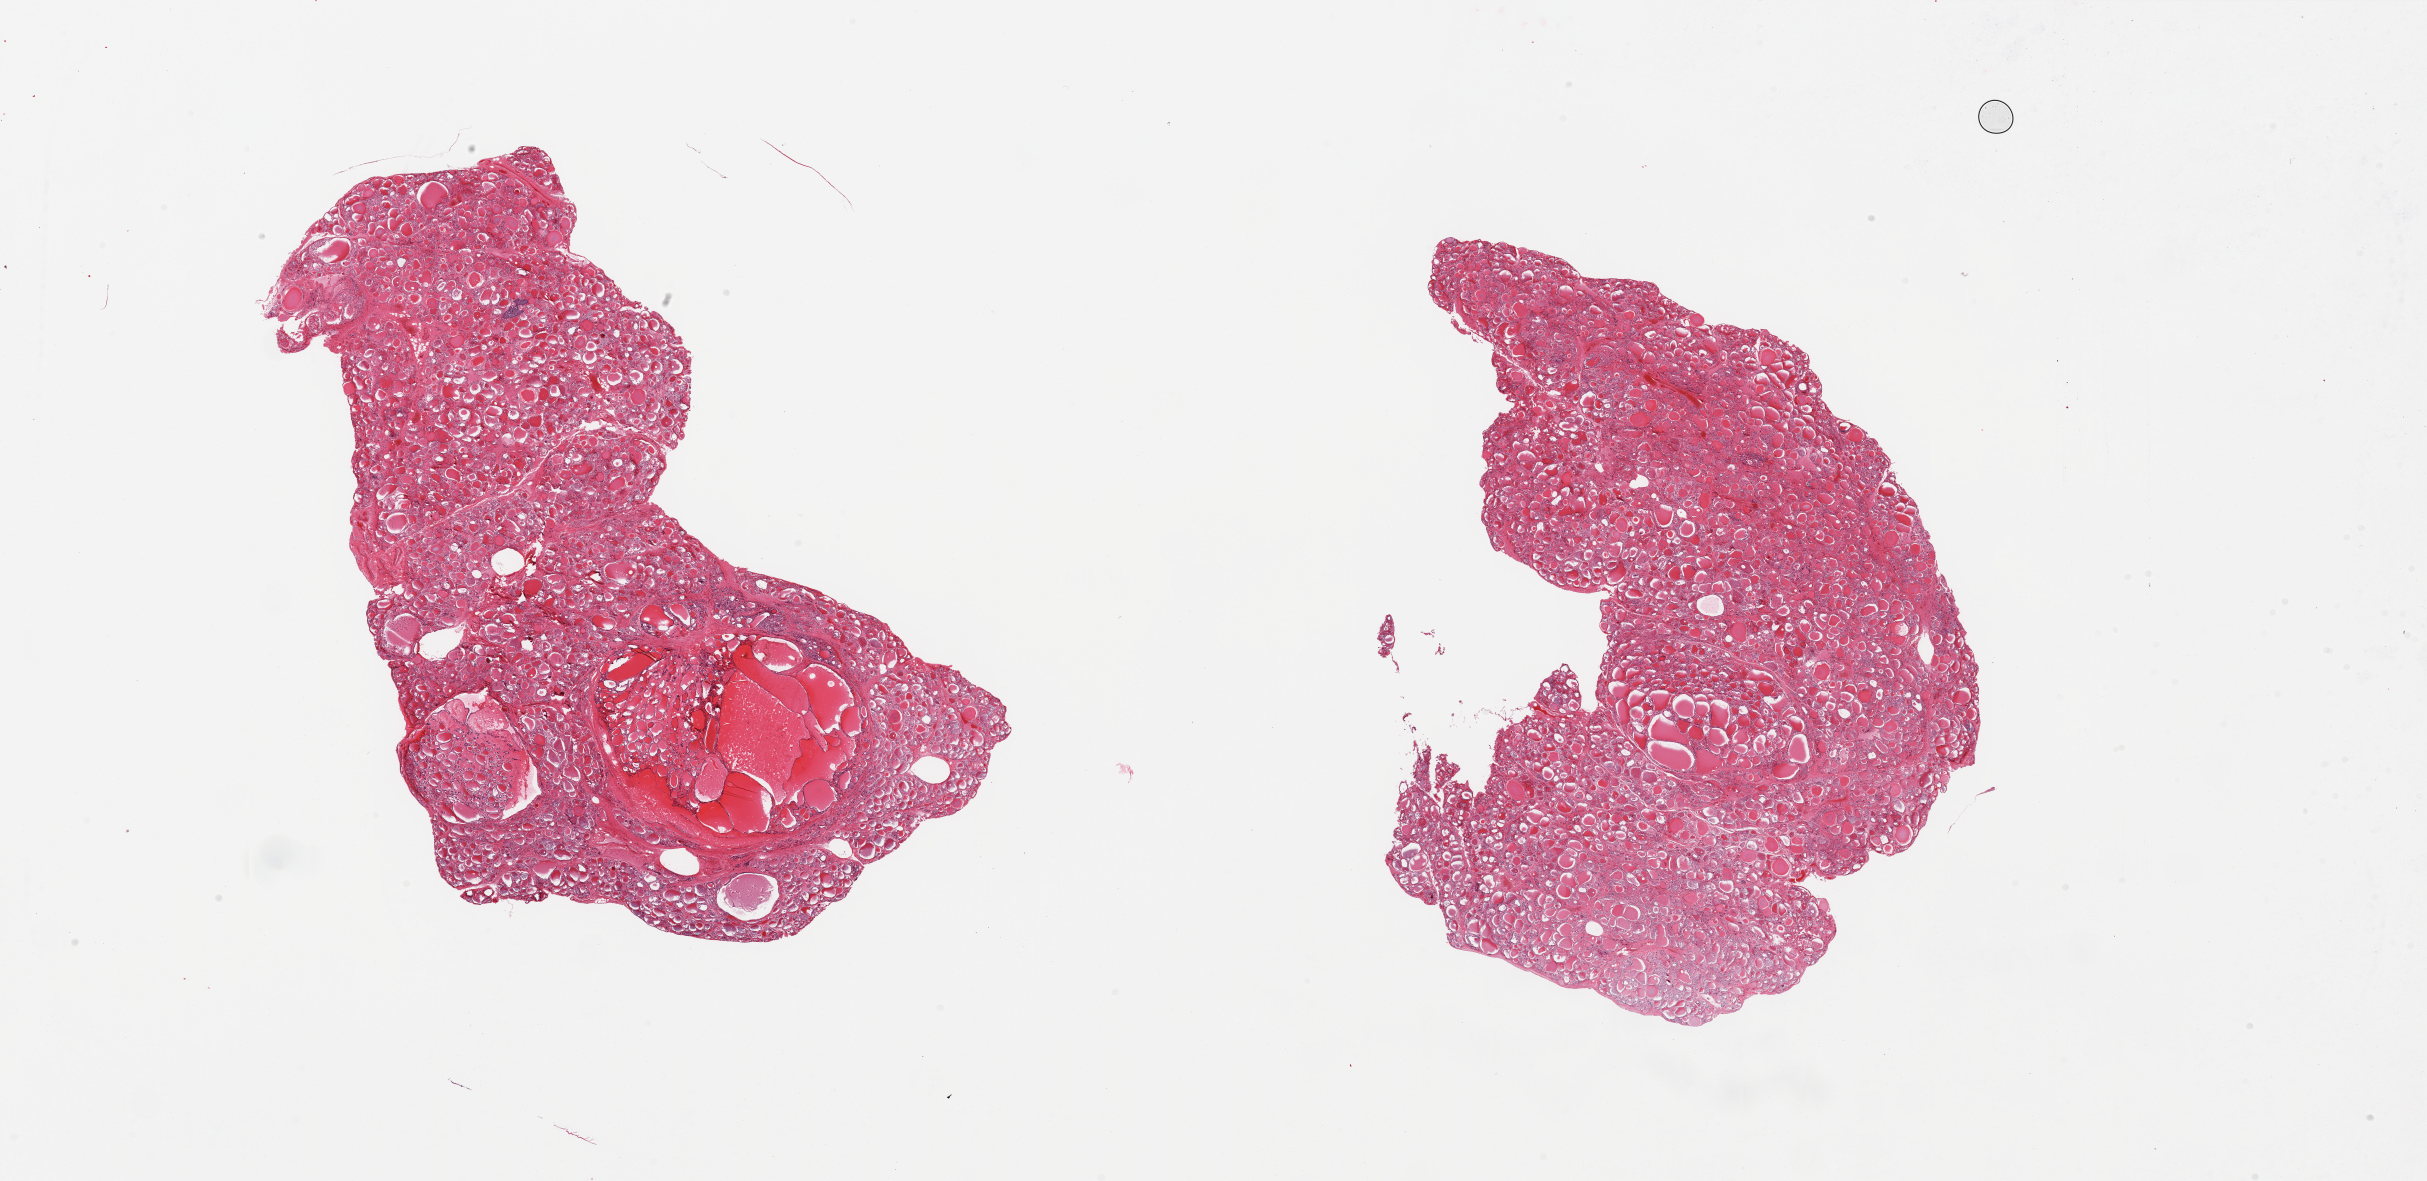
H&E whole-slide image, low-resolution overview of the scanned area, about 38.4 x 18.7 mm (from a 20x scan), PAXgene-fixed, paraffin-embedded tissue, target tissue: thyroid, tissue donor sample. Donor: male.
Reviewer comment on this tissue sample: 2 pieces; nodular goiter with focal solid cell nest.